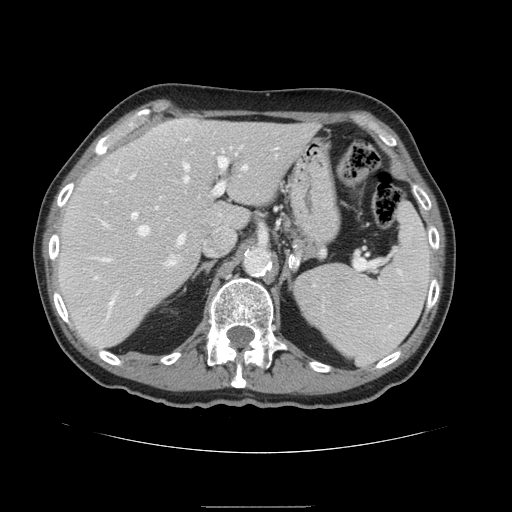
Contrast-enhanced abdominal CT, one axial slice. Position 102 of 168 along the scan axis. 120 kVp. Soft-tissue window (W 400 / L 40 HU). 2.5 mm slice thickness. 512 × 512 image matrix, field of view 386 × 386 mm. Male patient, age 74 years. From the clinical record (not read from this slice): diagnosis: colorectal cancer liver metastases, imaged before liver resection; multiple liver metastases: no; largest metastasis: 14.5 cm; disease in both lobes: yes.
Annotated regions visible in this slice (expert manual segmentation):
- hepatic veins: bounding box <106,163,247,305> (left, top, right, bottom; pixels)
- liver: <57,118,319,348>
- planned liver remnant (the part of the liver to remain after resection): <57,117,319,348>
- portal vein (with intrahepatic branches): <104,157,229,245>